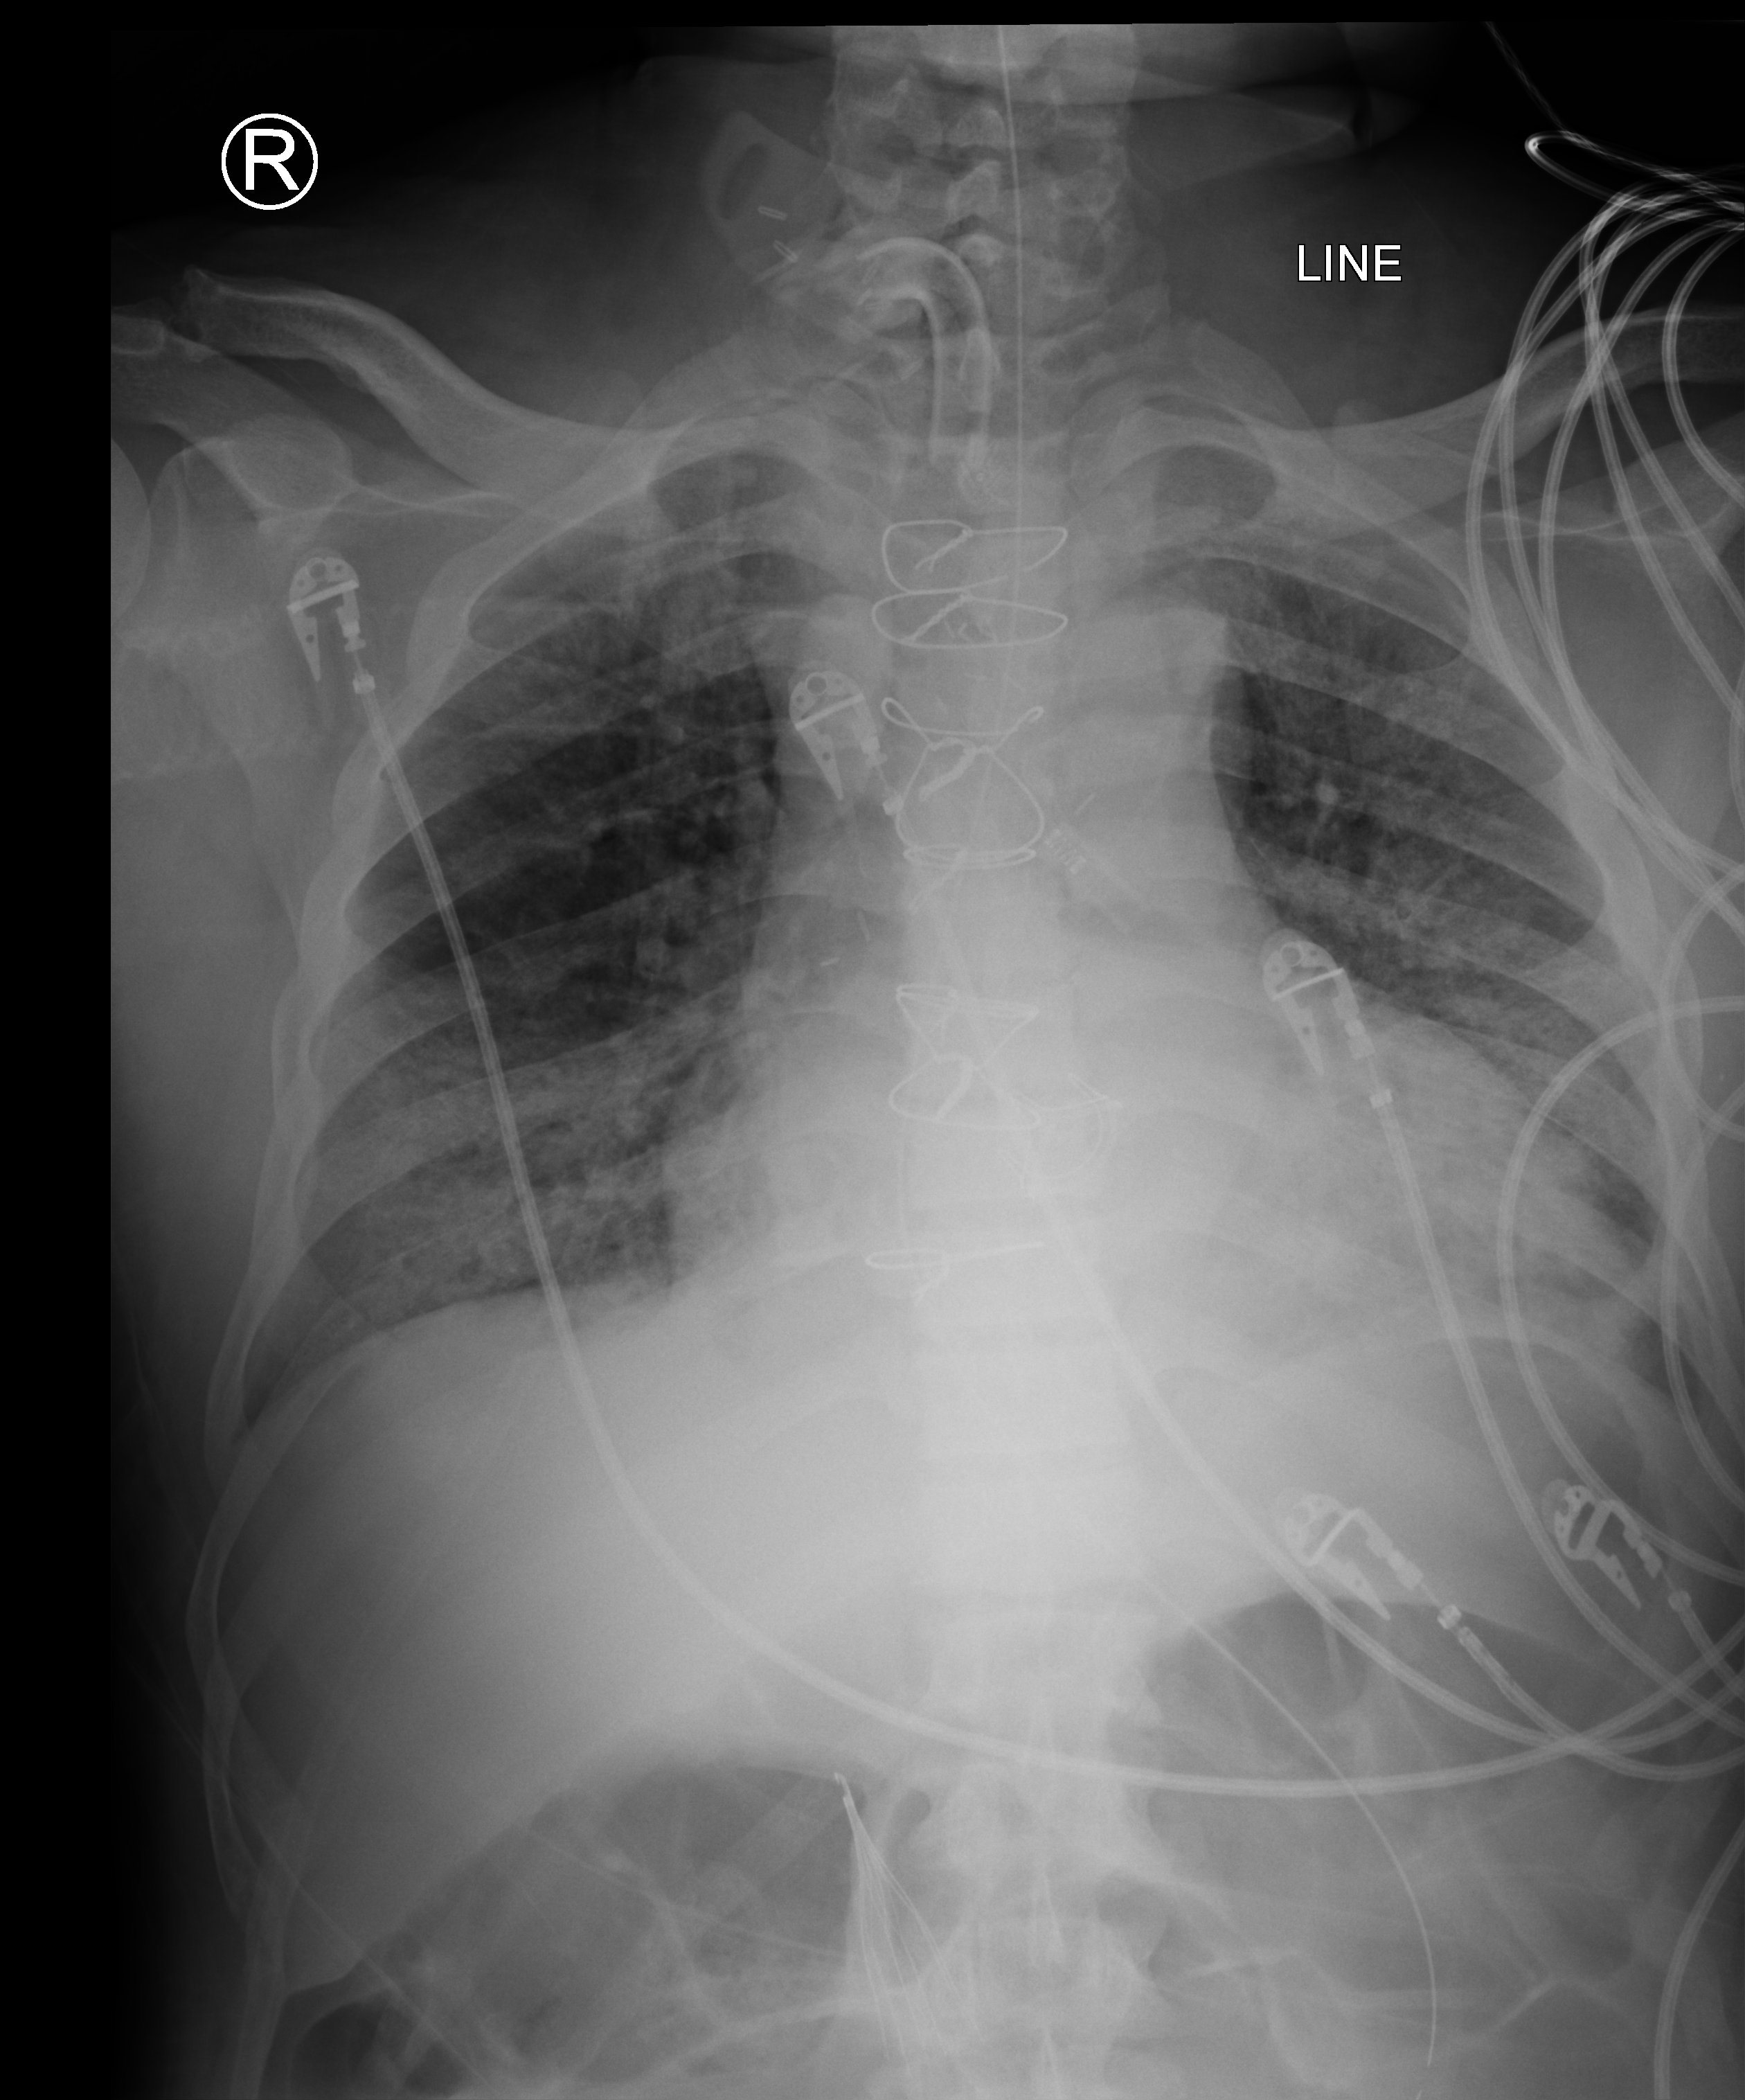
Bedside chest radiograph (computed radiography), anteroposterior (AP) projection. Male patient hospitalised with COVID-19, age 60–74 years.
From the hospital-stay record, not from the radiograph (when in the stay this image was taken is not recorded):
- mechanically ventilated during this hospital stay: yes